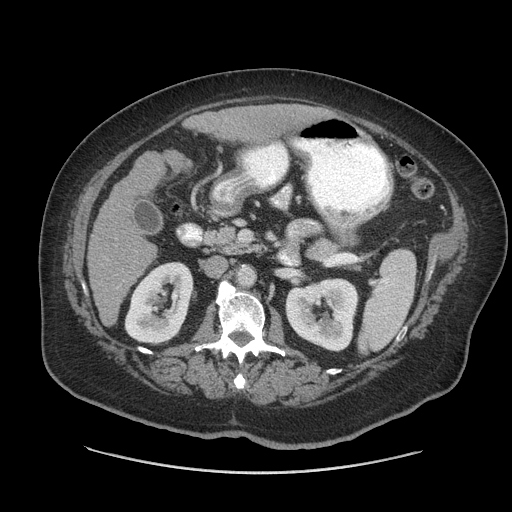
Contrast-enhanced abdominal CT (liver protocol), one axial slice; slice 25 of 91 in the series (ordered by position); reconstruction kernel STANDARD; 140 kVp; soft-tissue window (W 400 / L 40 HU); 512 × 512 image matrix, field of view 420 × 420 mm. Case-level facts recorded for this patient, not image findings: diagnosis: hepatocellular carcinoma (patient treated with transarterial chemoembolisation; whether this scan precedes or follows treatment is not stated here); TNM stage (as recorded): Stage-I; Child-Pugh class: A; tumour differentiation: well differentiated; tumour nodularity: uninodular.
Structures marked on this image (semi-automatic segmentation, software-assisted and operator-edited):
- liver parenchyma outside the tumour (the mass and vessels are separate outlines, so this box may not span the whole liver): bounding box <88,104,320,324> (left, top, right, bottom; pixels)